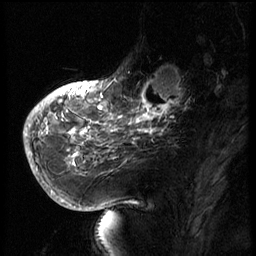
Breast MRI (dynamic contrast-enhanced), one sagittal slice; slice 18 of 66 in the series (ordered by position); 3 images stored at this slice position (order not interpretable as contrast timing); 1.5 T; TE 4.2 ms, TR 8.9 ms; 256 × 256 image matrix. Patient: female, 56 years. Case-level facts recorded for this patient, not image findings: setting: breast cancer imaged before/during neoadjuvant chemotherapy.
Structures marked on this image (semi-automatically segmented with operator editing):
- analysis volume of interest (the breast-tissue region the enhancement analysis was run in; not a lesion): box from (x=129, y=62) to (x=194, y=127) px
- tumour enhancement mask (voxels above the 140 % enhancement threshold inside the analysis volume of interest): (x=130, y=82)–(x=188, y=127)